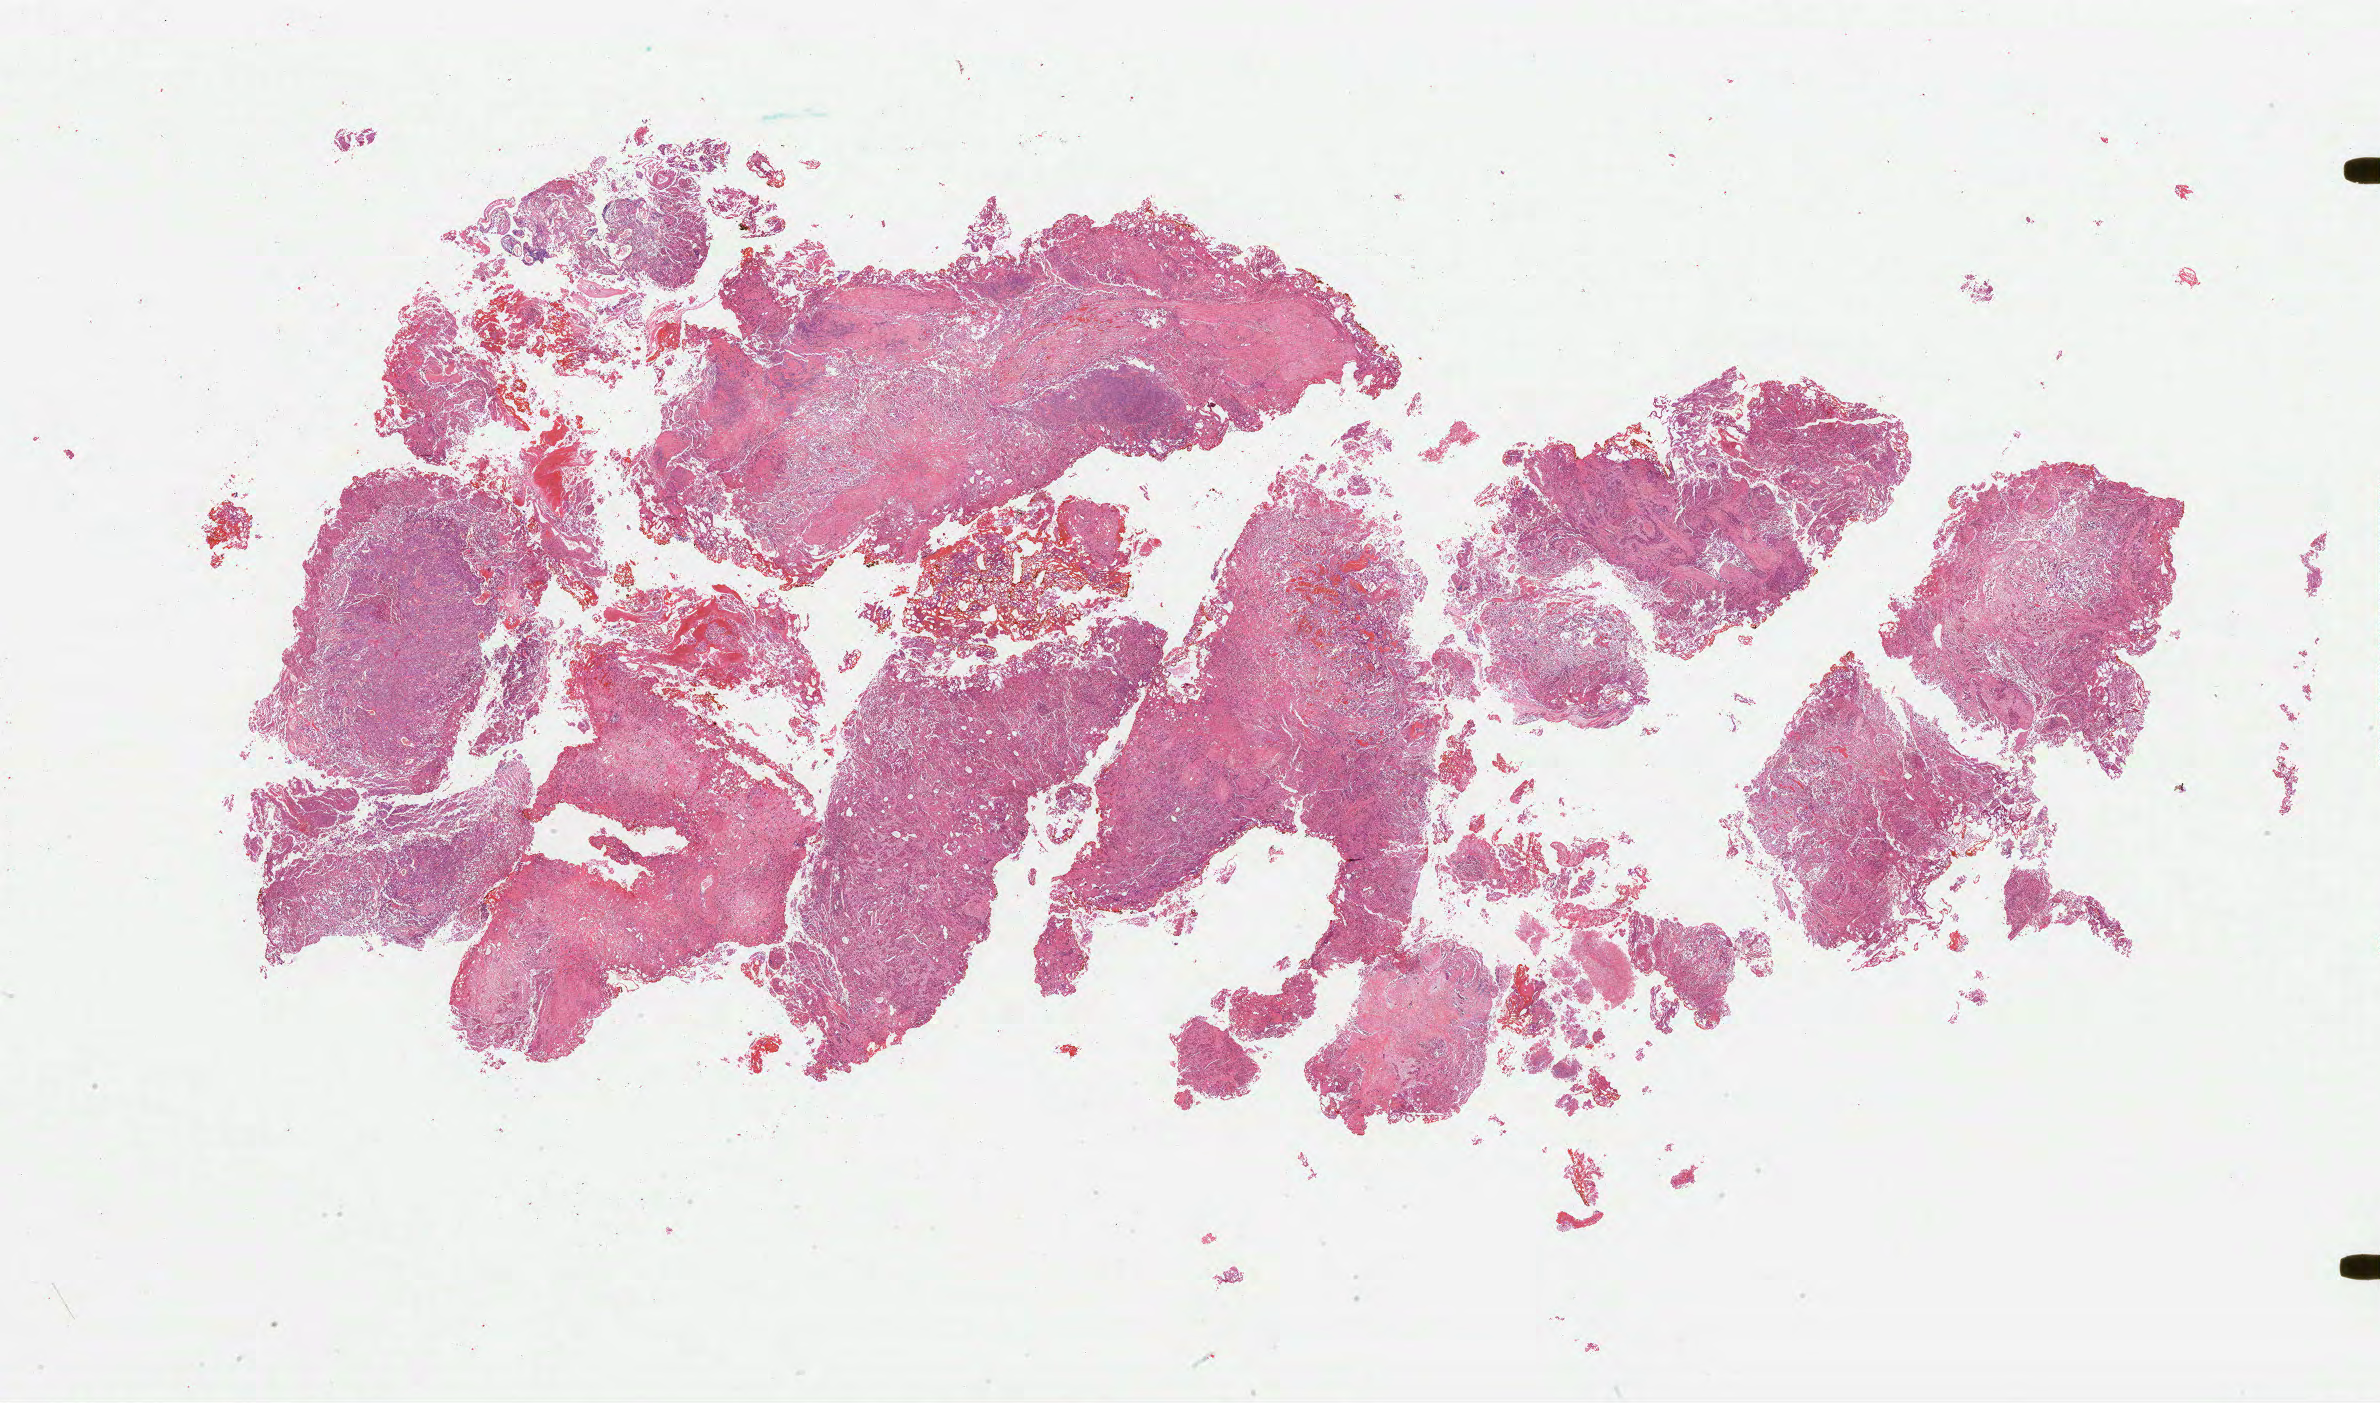
H&E-stained whole-slide image — whole scanned area (about 37.8 x 22.3 mm) shown as a low-resolution overview. Formalin-fixed paraffin-embedded (FFPE) diagnostic section. Bladder, primary tumour sample. Male, age 75 years at initial diagnosis. Histologic grade: high grade.
AJCC pathologic stage: II. TNM: NX MX. Diagnosis: Transitional cell carcinoma.